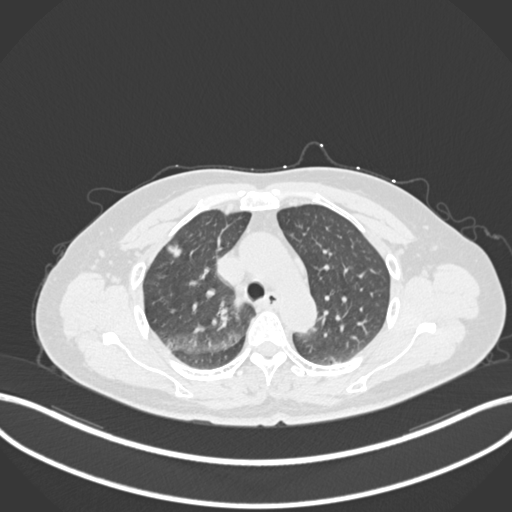
Chest CT, one axial slice; position 165 of 223 along the scan axis; reconstruction kernel B30f; 120 kVp; lung window (W 1500 / L -600 HU); 1 mm slice thickness; 512 × 512 image matrix, field of view 400 × 400 mm. Female patient, age 56 years. From the clinical record (not read from this slice): clinical TNM (as recorded): T1c N0 M0.
Annotated regions visible in this slice (rectangle marked by the reading radiologist):
- lung tumour (recorded histology: adenocarcinoma): bounding box [x1, y1, x2, y2] px = [166, 241, 184, 263]